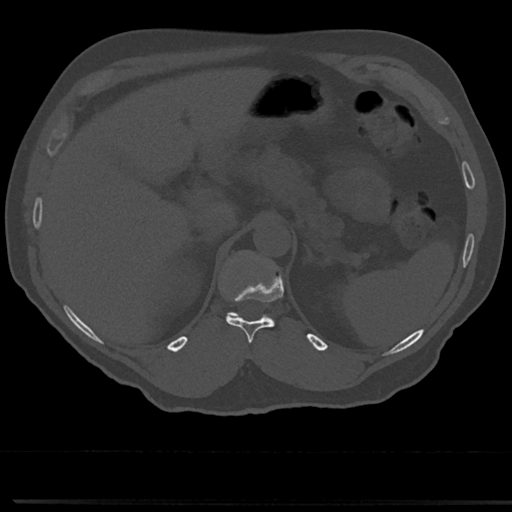
CT including the spine, one axial slice. Position 186 of 817 along the scan axis. 120 kVp. Bone window (W 1800 / L 400 HU). 0.5 mm slice thickness. 512 × 512 image matrix. Patient: male, 61 years. From the clinical record (not read from this slice): primary cancer: prostate.
Annotated regions visible in this slice (semi-automatically segmented with operator editing):
- T11 vertebra: bounding box (x1, y1, x2, y2) in pixels: (226, 289, 281, 345)
- T12 vertebra: (225, 251, 276, 320)